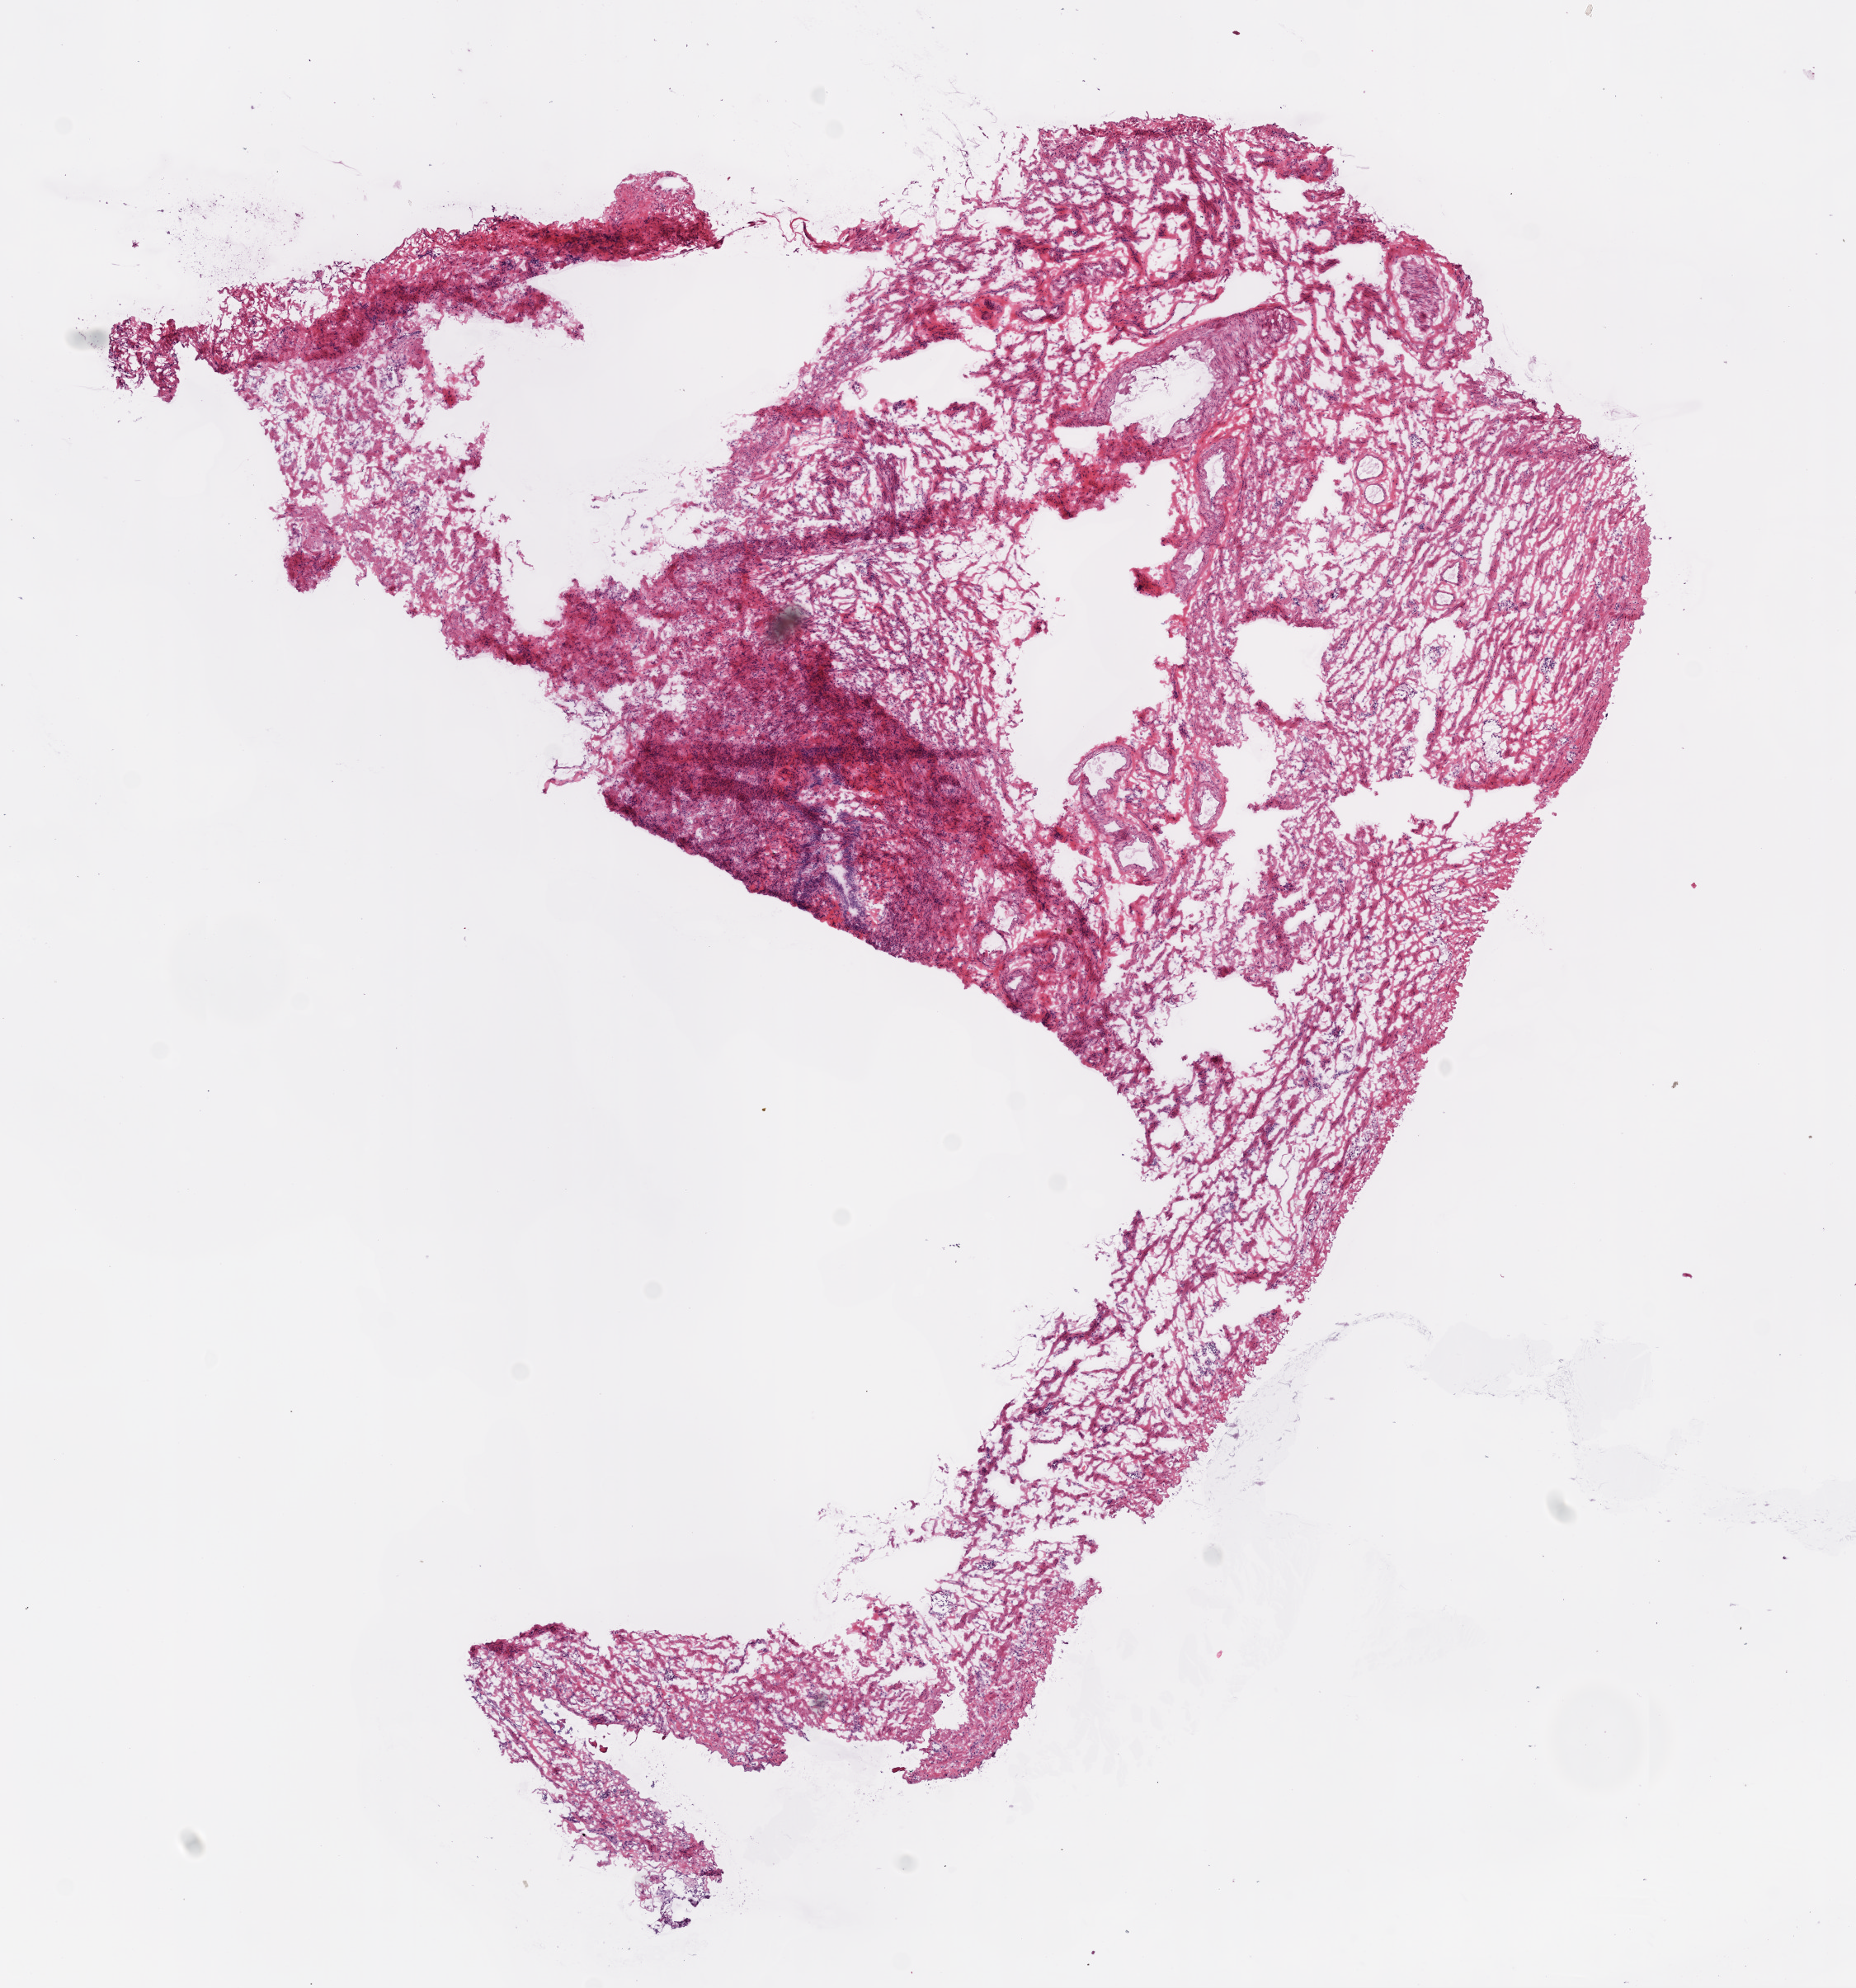
Whole-slide histology image, H&E, shown as a low-resolution overview of the whole scanned area (about 9.0 x 9.7 mm, from a 20x scan), frozen section, solid tissue normal (non-tumour tissue) sample from the ovary. Female patient; age at initial diagnosis 56 years.
This section: solid tissue normal sample (biorepository sample class). Patient diagnosis: Serous cystadenocarcinoma, NOS.